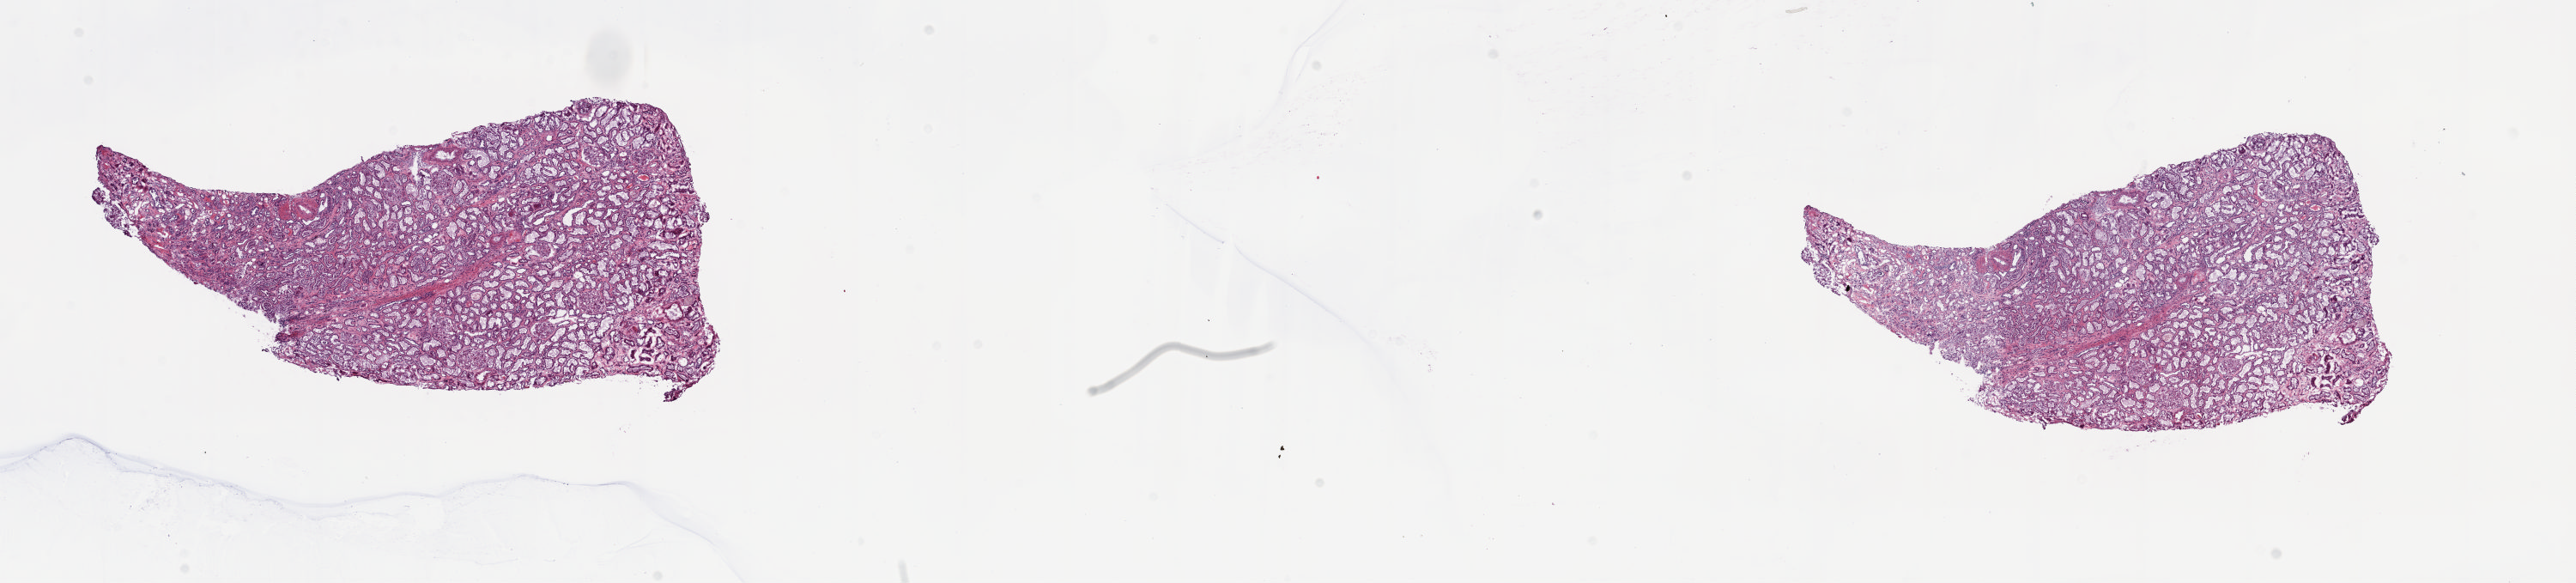
Whole-slide histology image, H&E-stained — whole scanned area (about 23.8 x 5.4 mm, slide scanned at 20x) shown as a low-resolution overview, frozen section from the top of the tissue portion, sample: solid tissue normal (non-tumour tissue), kidney. Male, age 61 years at initial diagnosis. Composition of this section per pathologist review: tumour cells 0%, tumour nuclei 0%, normal cells 65%, stromal cells 35%, necrosis 0%. Inflammatory infiltration, as recorded: lymphocyte infiltration 2%, monocyte infiltration 1%, neutrophil infiltration 1%.
• this section: solid tissue normal sample (biorepository sample class)
• patient diagnosis: Papillary adenocarcinoma, NOS